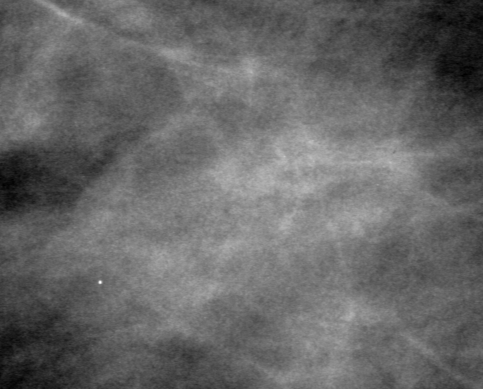
Region of interest cut from a scanned film mammogram (one marked finding), right breast, MLO view.
Marked abnormality: mass, shape oval, margins obscured; BI-RADS assessment category 0 (incomplete: needs additional imaging); pathology (as recorded): benign.